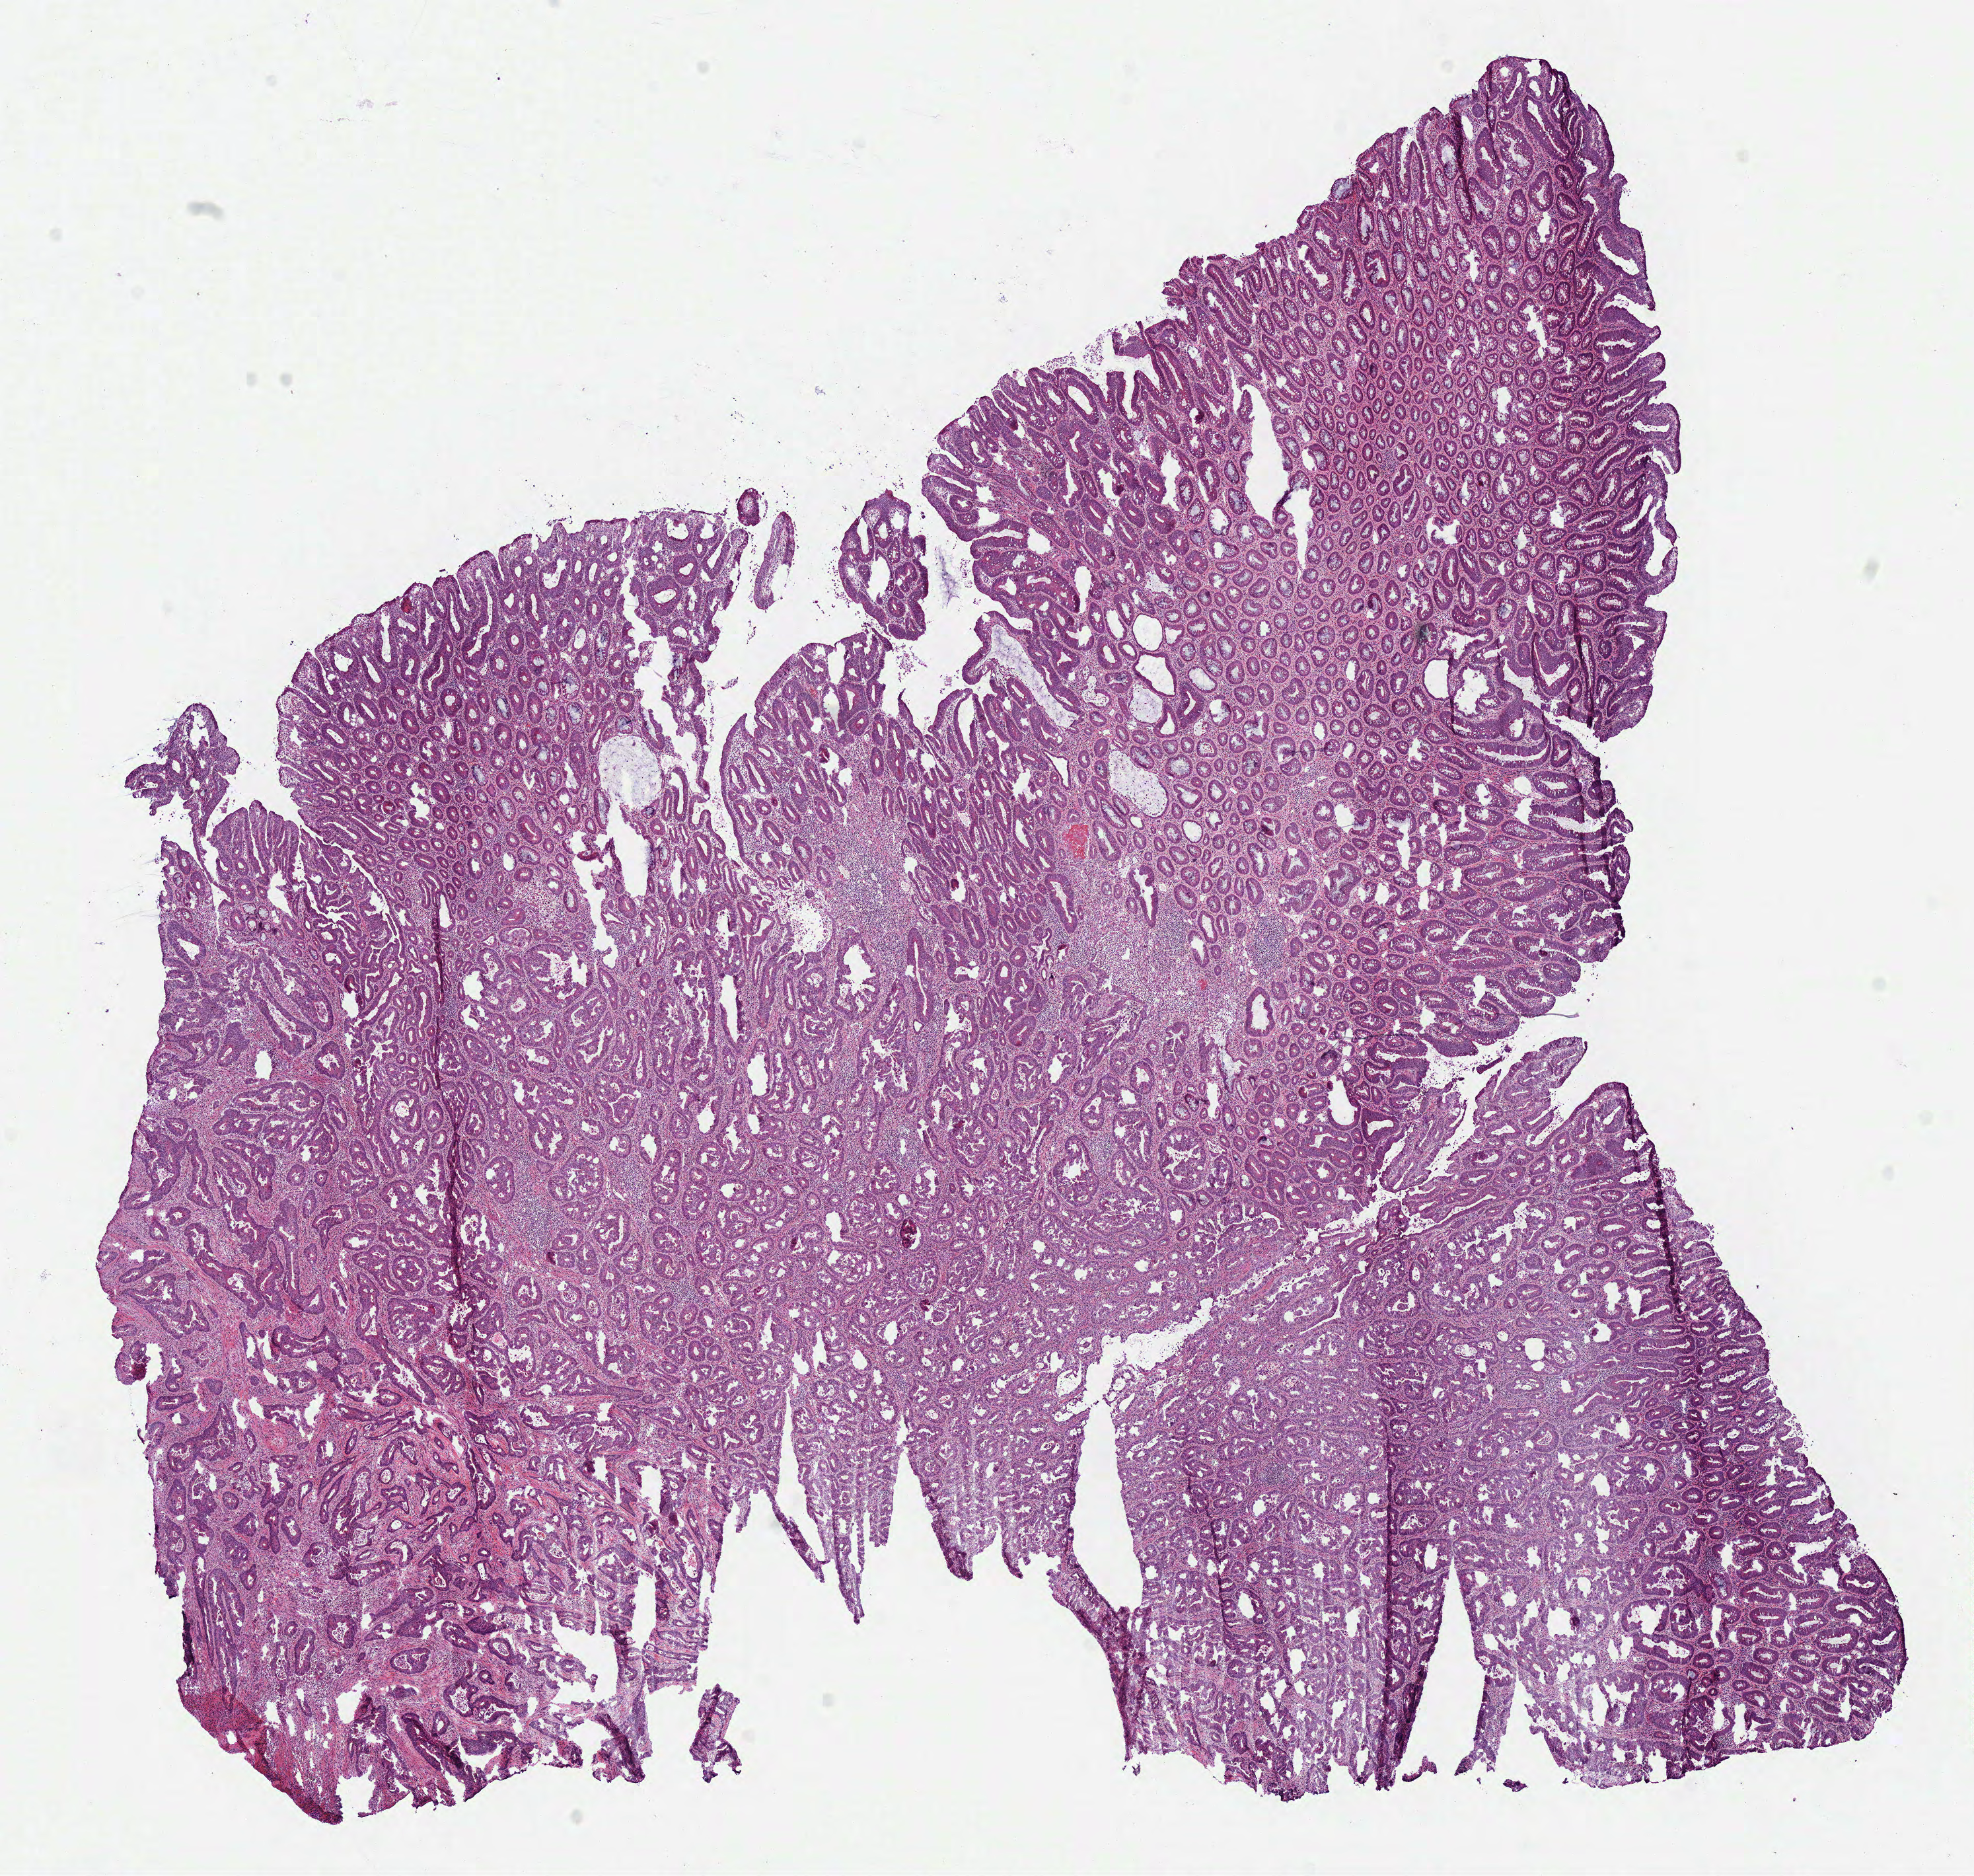
Hematoxylin and eosin (H&E) stained whole-slide image — a low-resolution overview of the entire scanned area, about 11.7 x 11.2 mm, frozen section from the bottom of the tissue portion, colon, primary tumour sample. Patient: female, age at initial diagnosis 72 years. Slide review estimates, as recorded: tumour cells 60%, tumour nuclei 65%, normal cells 25%, stromal cells 10%, necrosis 5%.
* pathologic diagnosis: Adenocarcinoma, NOS (descending colon)
* lymph nodes positive (case pathology): 0 of 12 examined
* AJCC pathologic stage: I (7th edition)